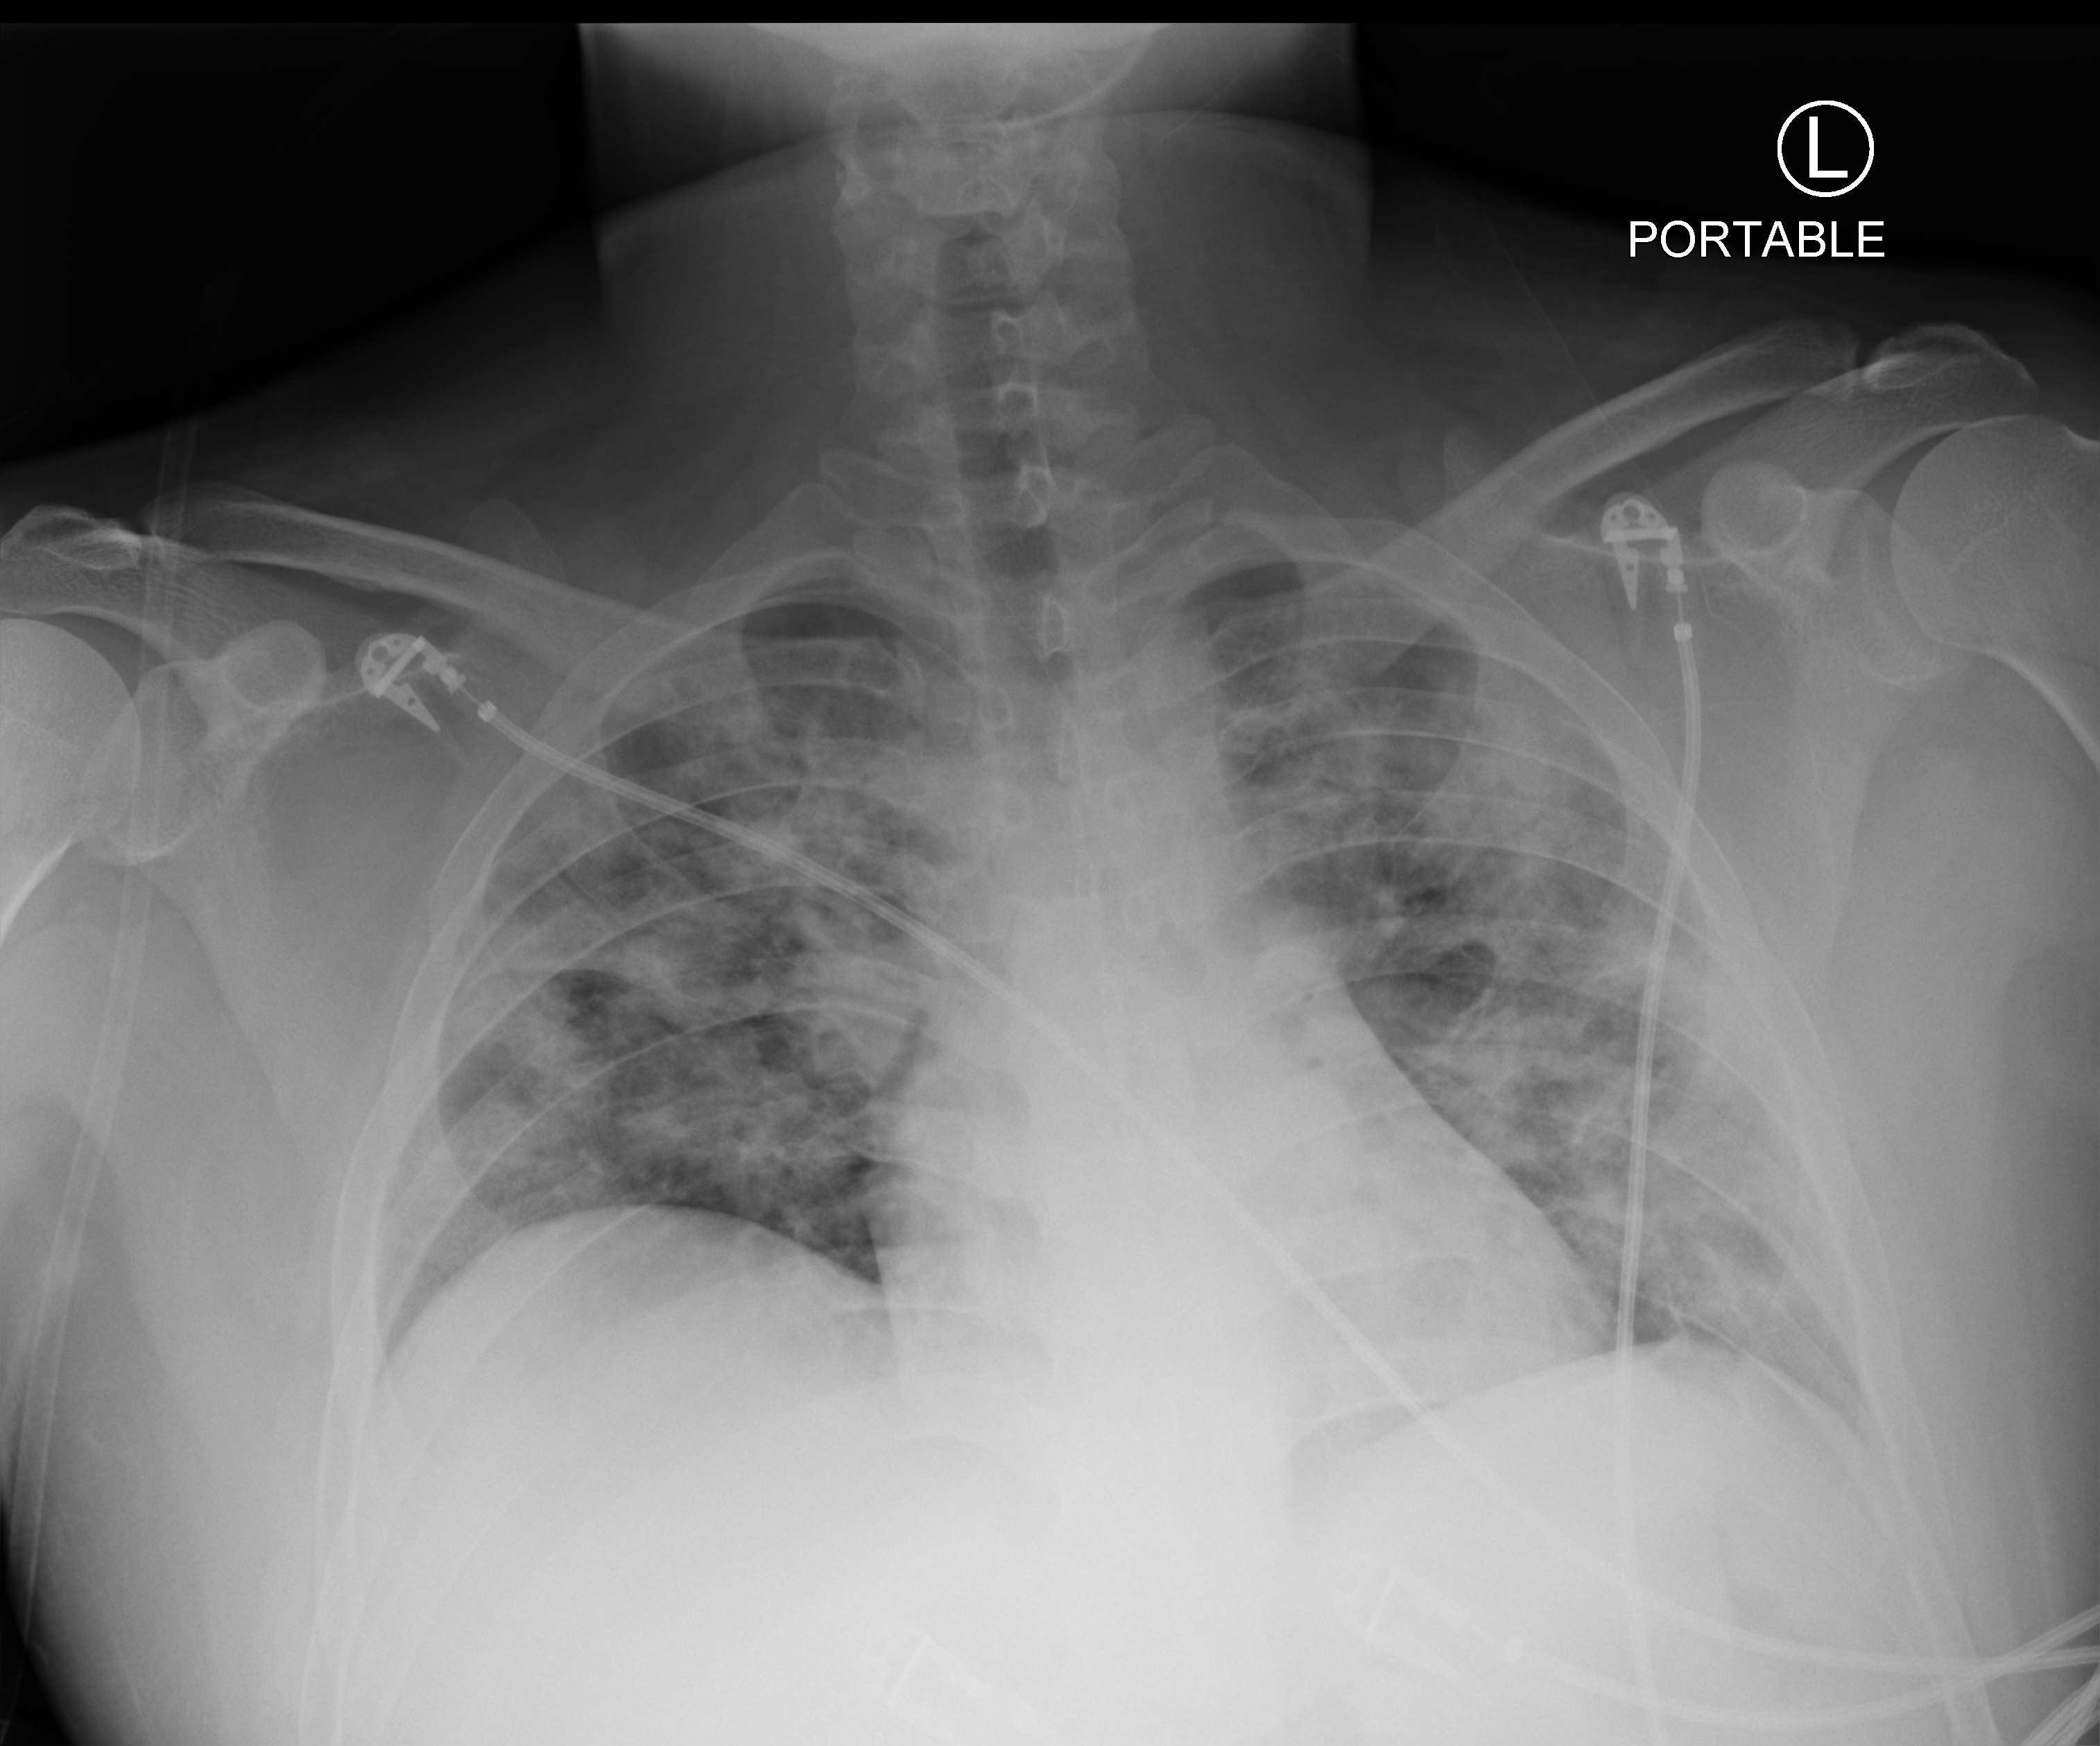
Portable chest radiograph, anteroposterior (AP) projection. Patient hospitalised with COVID-19; male, aged 18–59 years.
Admission-level facts for this patient (not findings on this image; timing relative to this image not recorded):
- mechanically ventilated during this hospital stay: yes
- length of hospital stay: 44 days
- admitted to intensive care during this hospital stay: yes